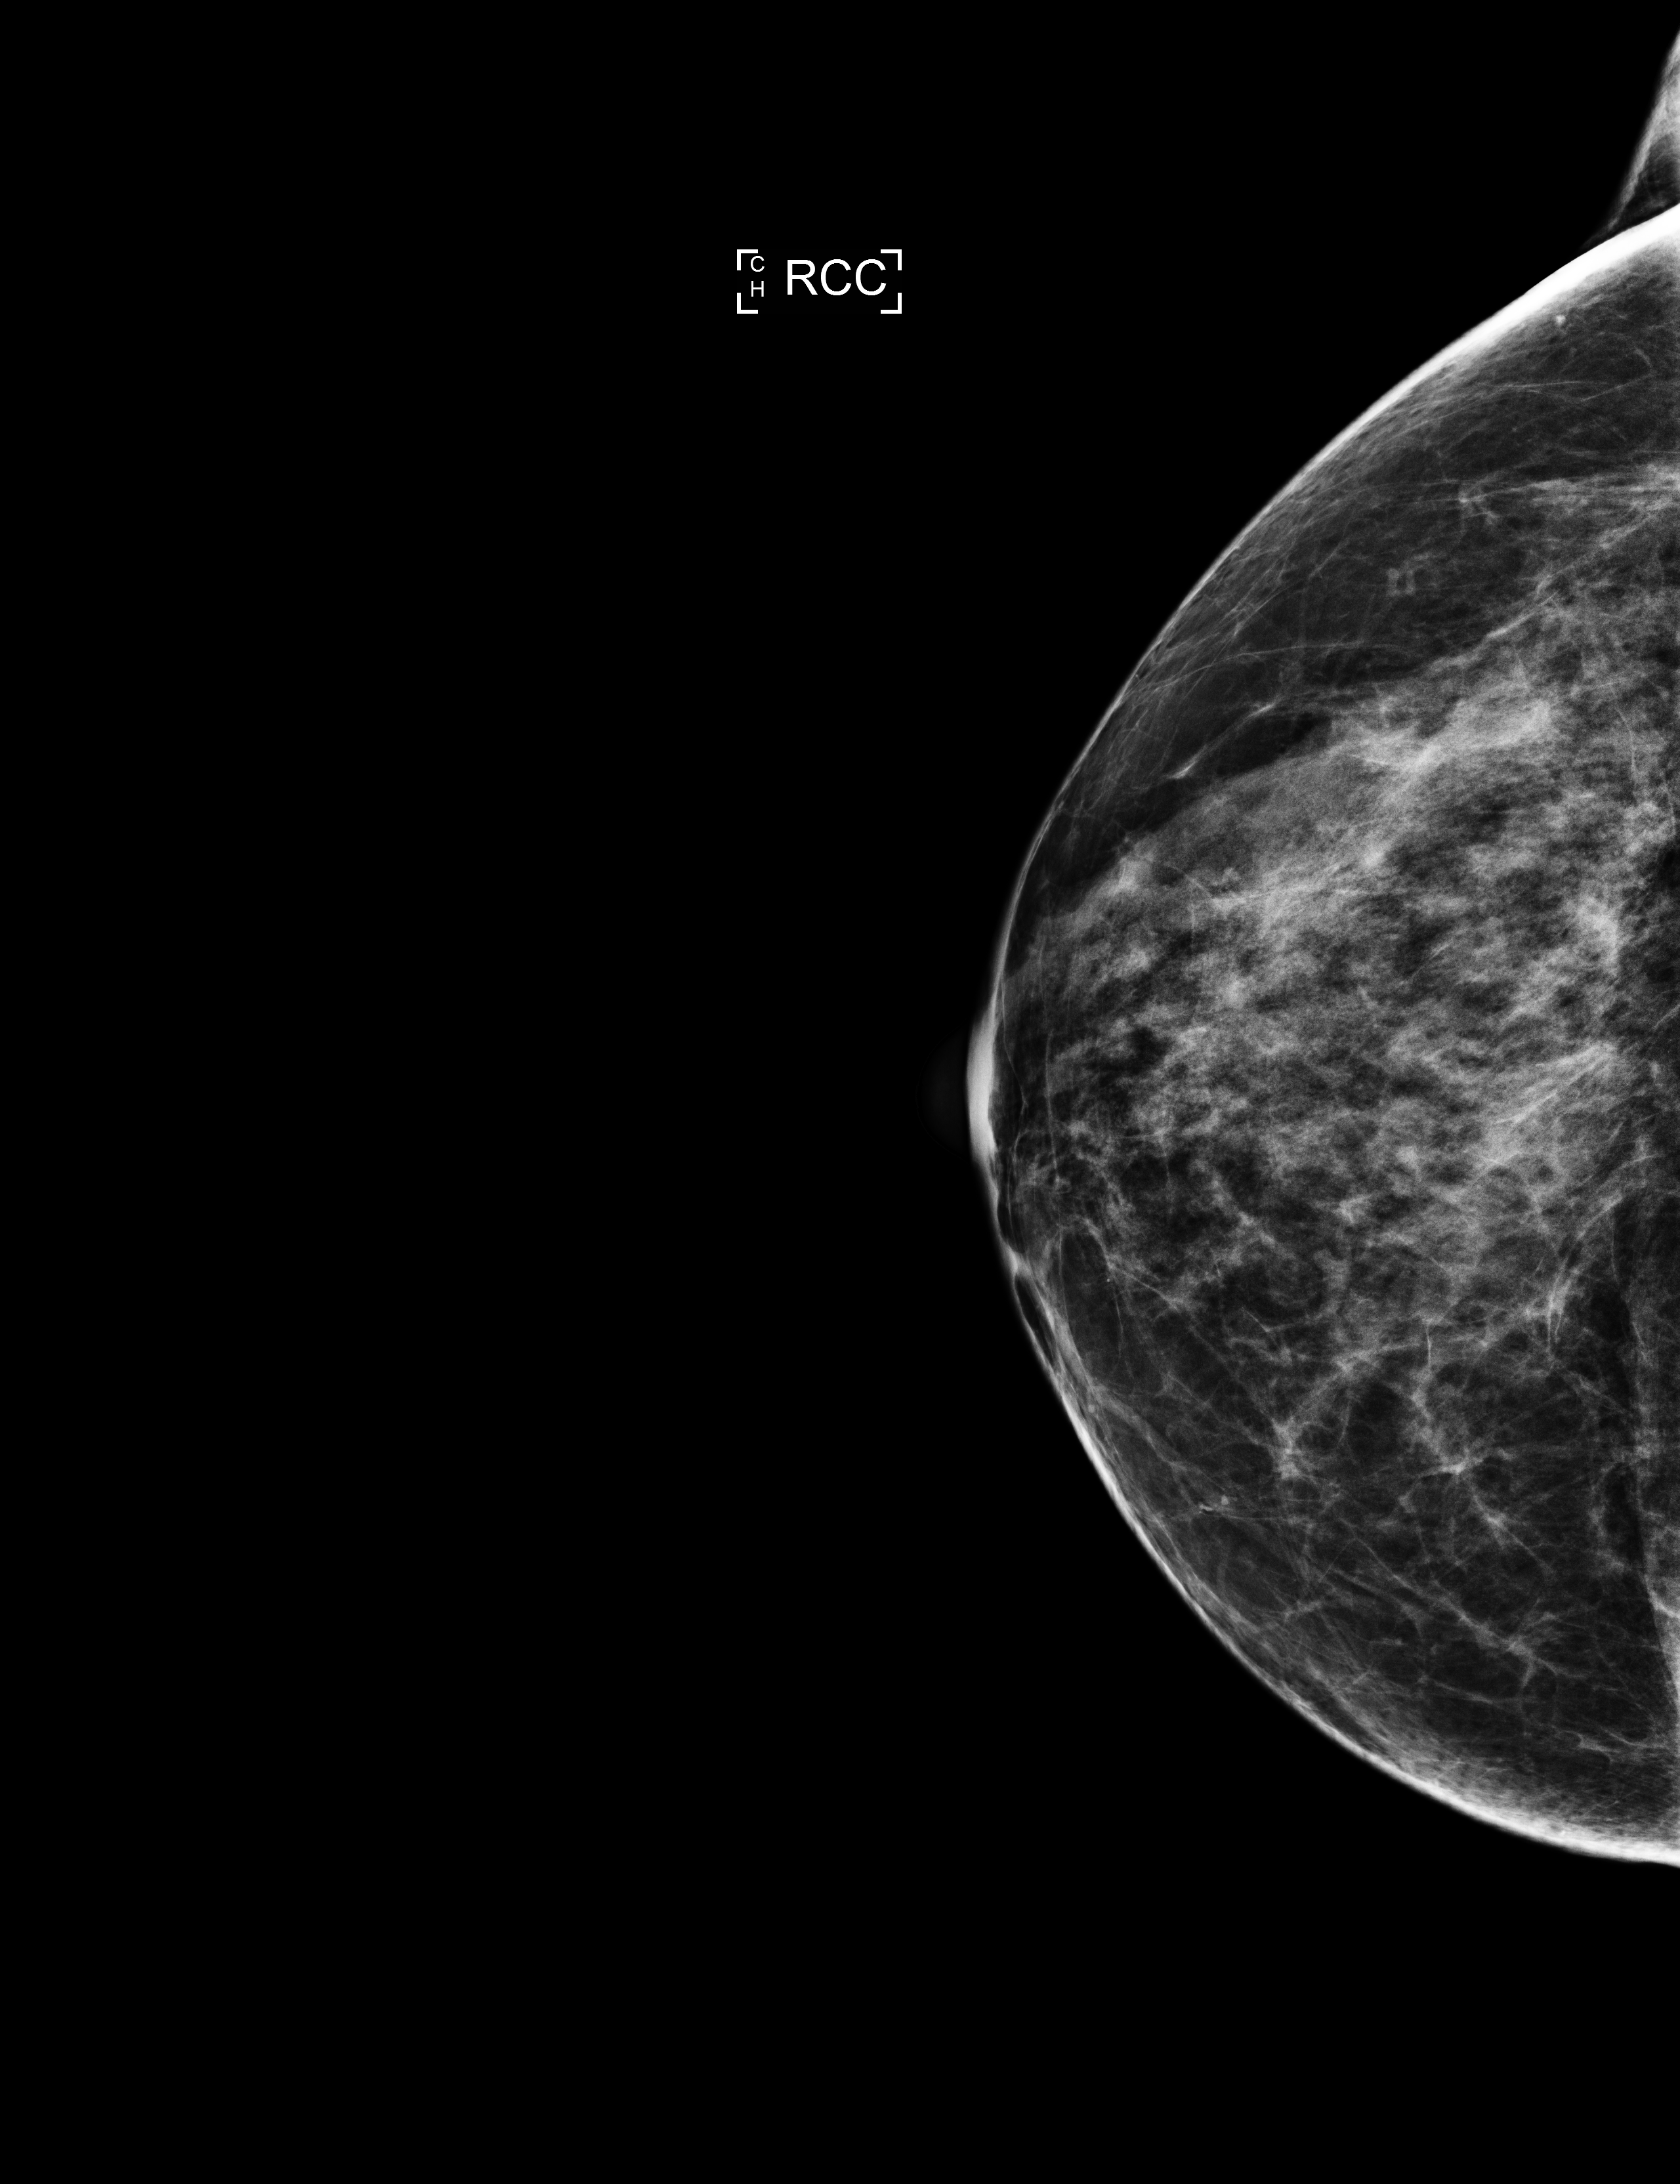
Screening examination; compressed breast thickness 57 mm. Patient: female, 60 years.
Image type: full-field digital mammogram. Breast: right. Projection: cranio-caudal projection.